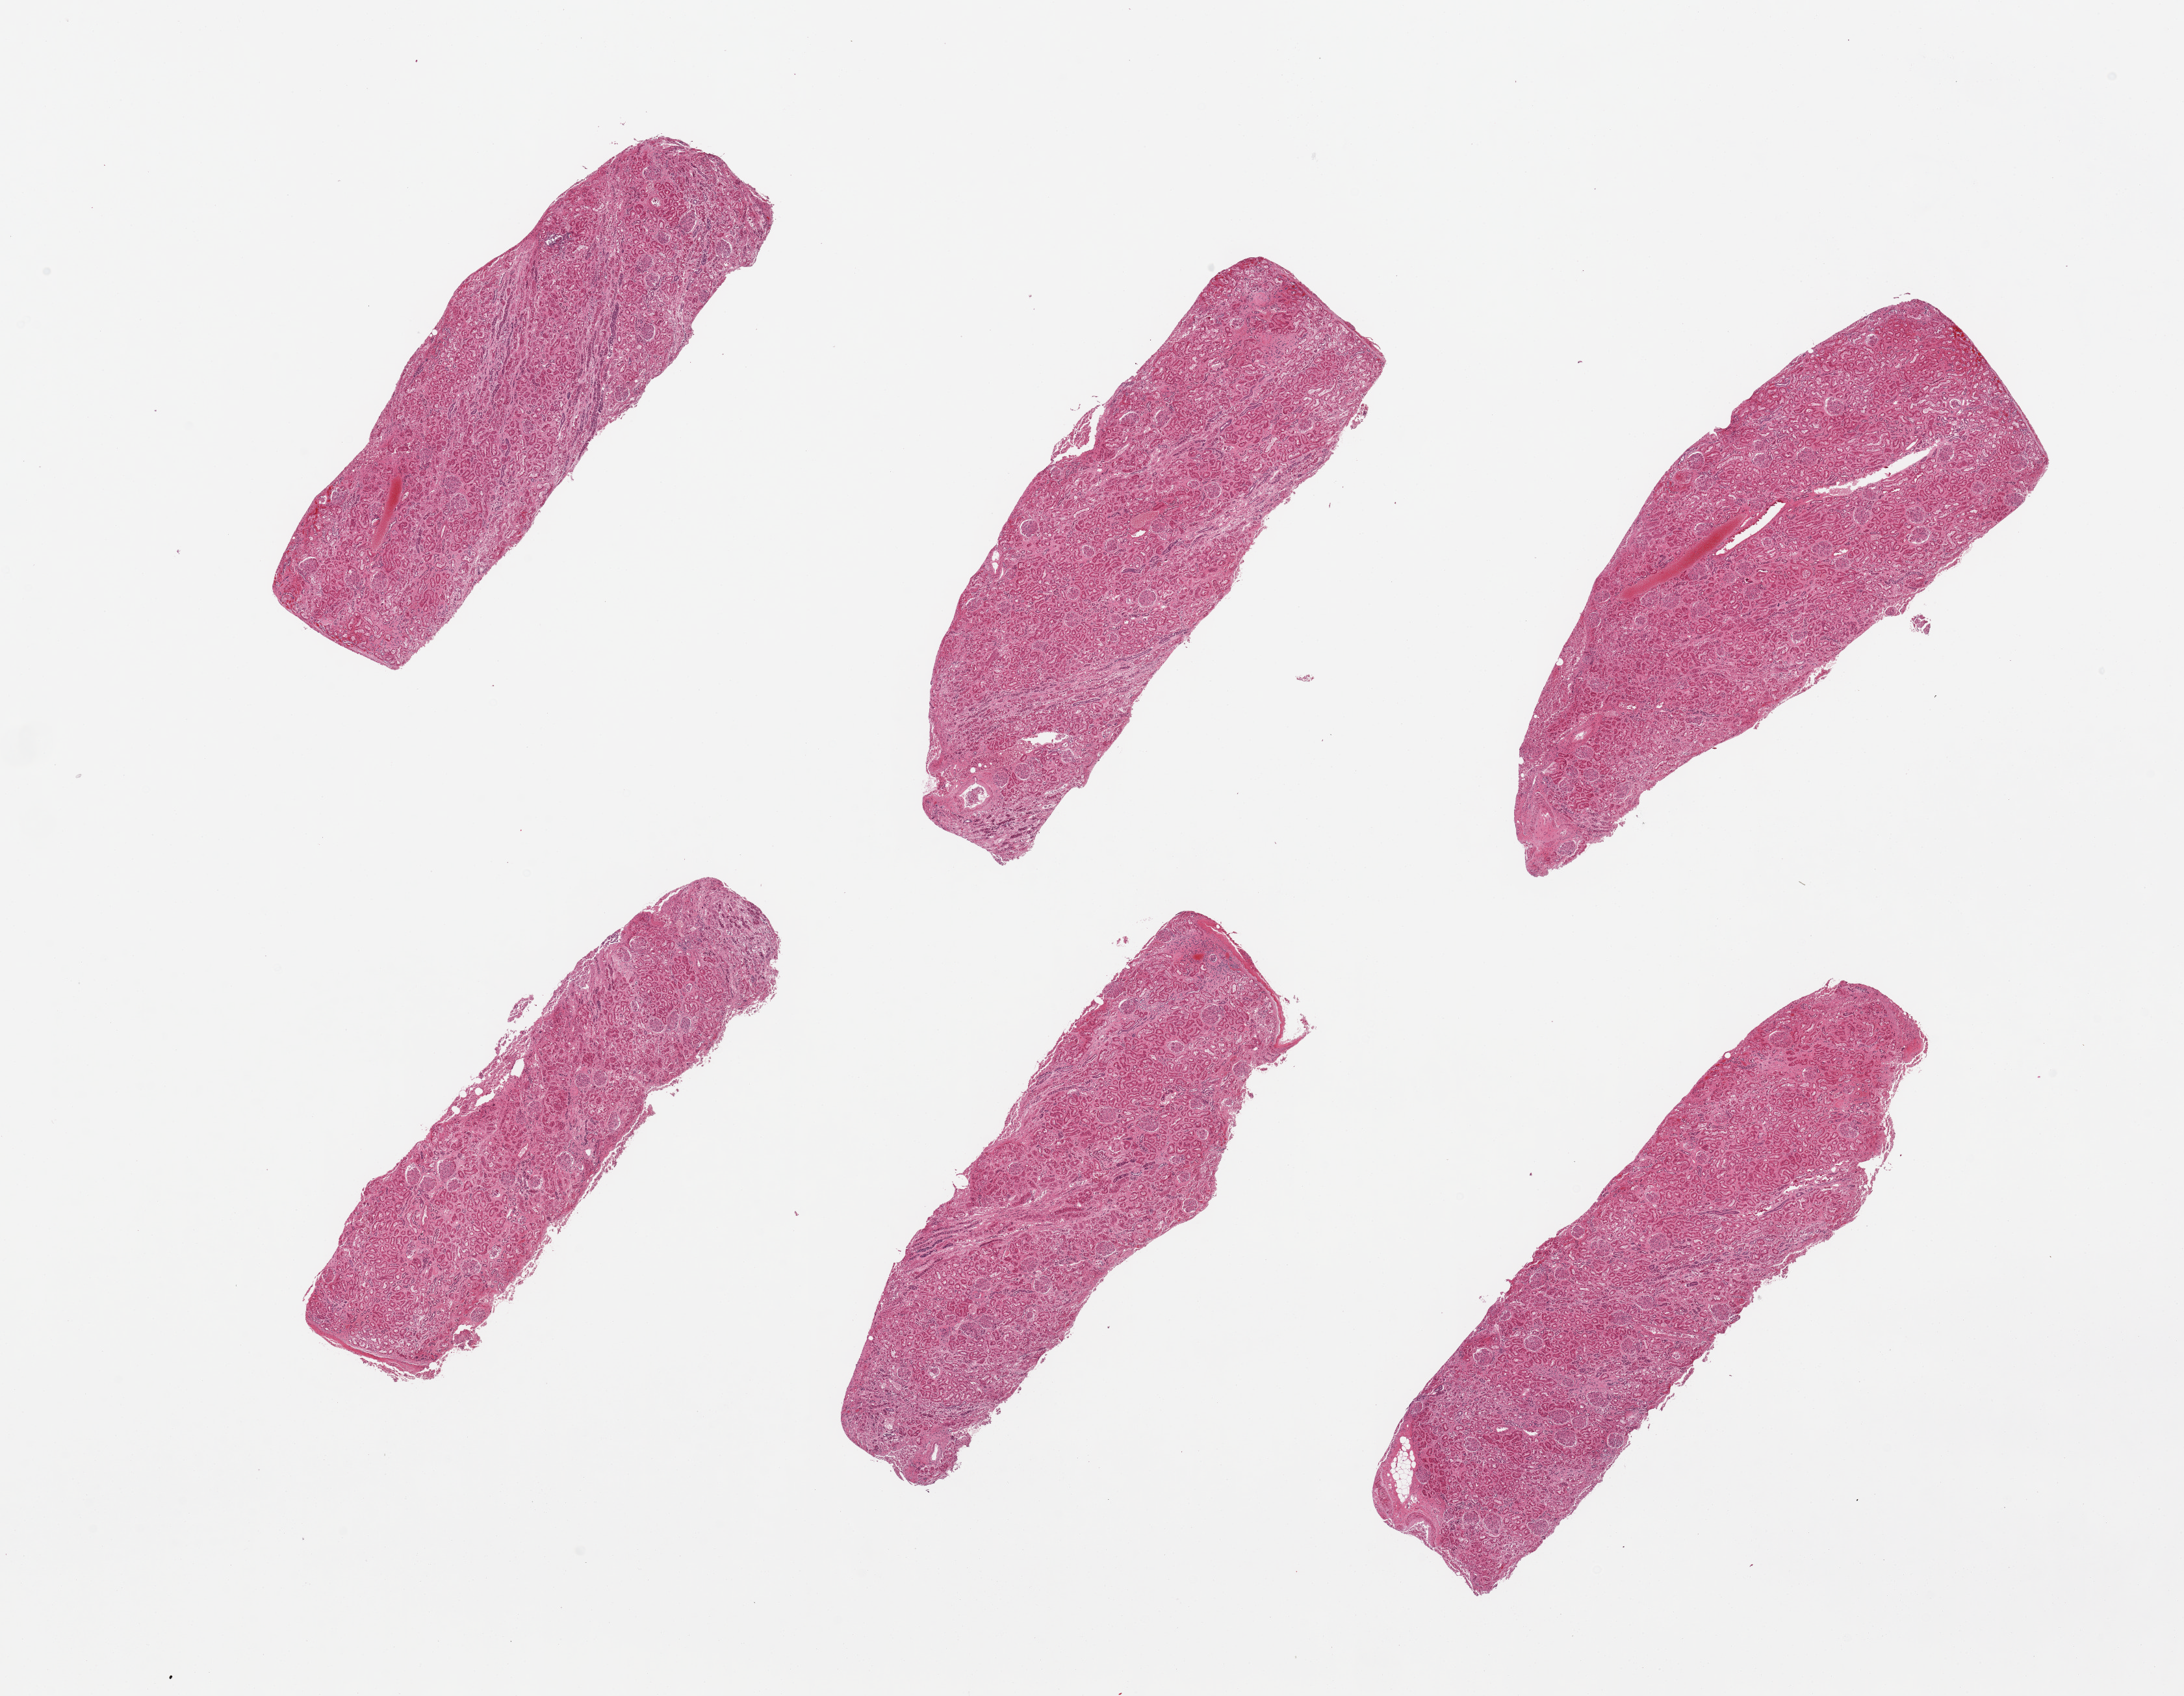
Digitized hematoxylin and eosin (H&E)-stained section, brightfield, low-resolution overview of the scanned area, about 26.6 x 20.6 mm; PAXgene-fixed paraffin-embedded (PFPE) section; sampled site (target tissue): renal cortex; donor tissue sample. Female donor.
Pathologist's review note for this sample: 6 pieces, all have glomeruli.